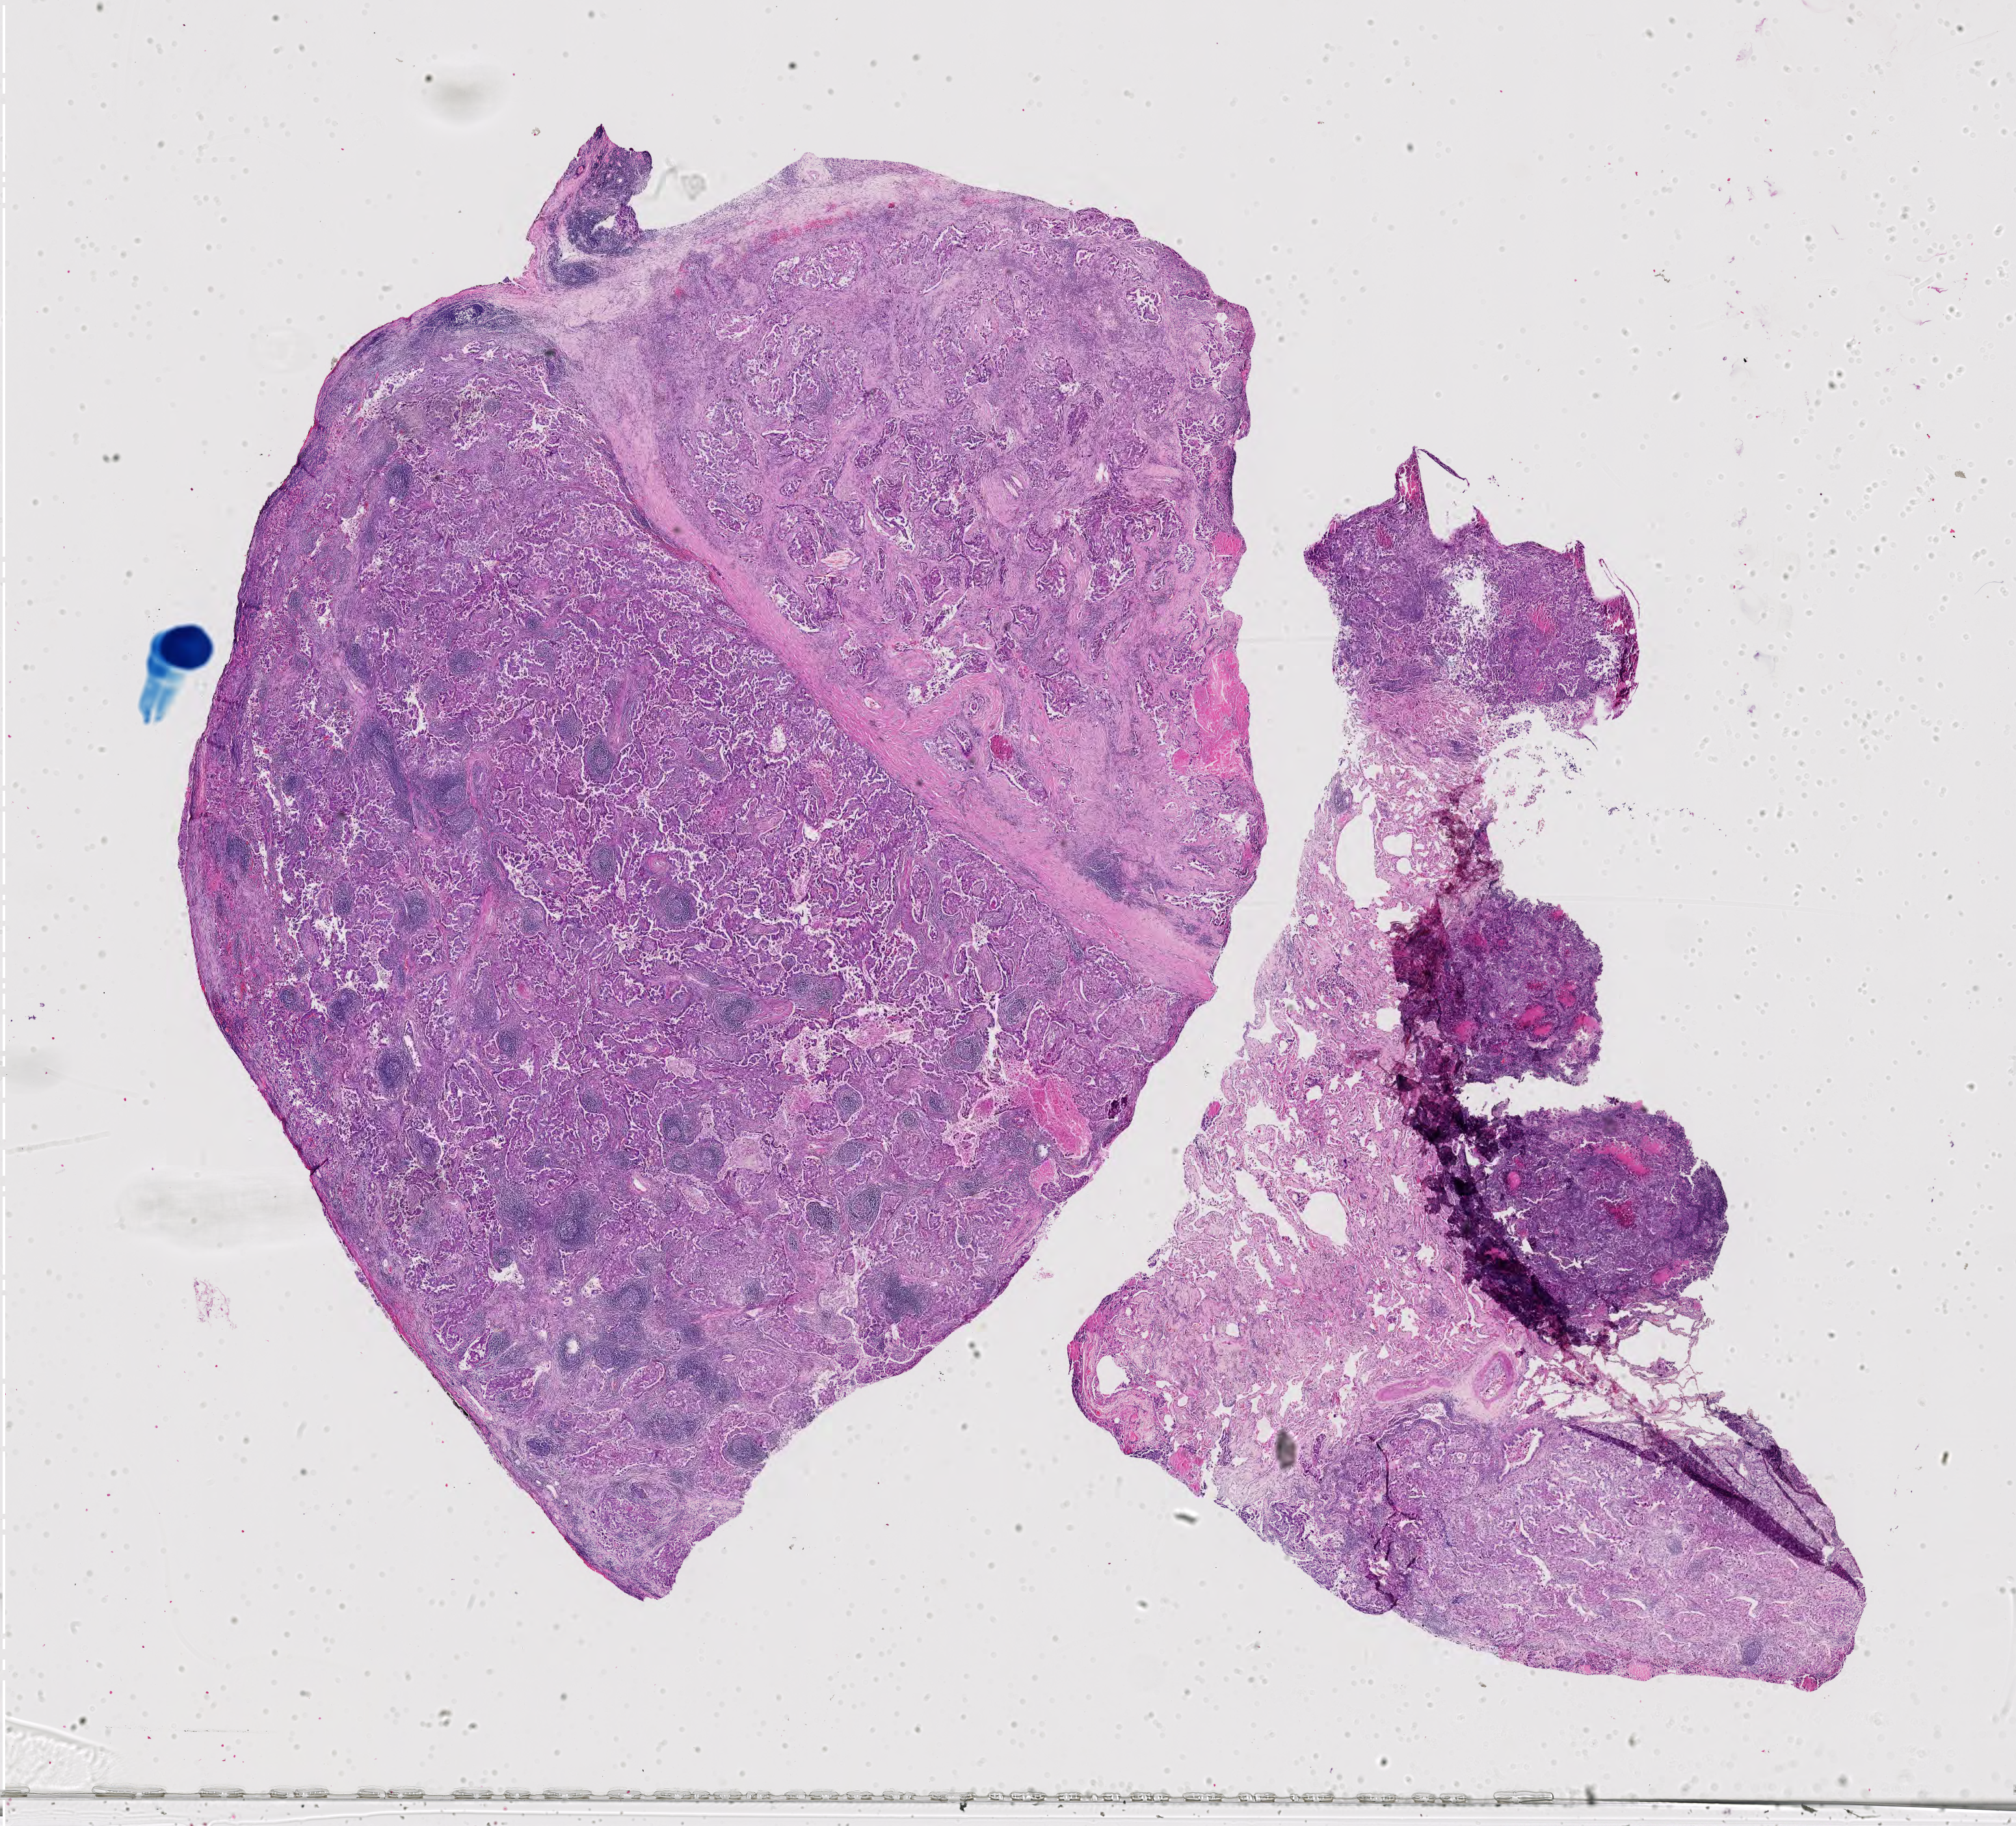
H&E whole-slide image, whole scanned area (about 22.5 x 20.4 mm, acquisition: 40x scan) shown as a low-resolution overview; formalin-fixed paraffin-embedded (FFPE) diagnostic section; primary tumour sample from the lung. Male patient; age at initial diagnosis 61 years.
Diagnosis: Adenocarcinoma with mixed subtypes.